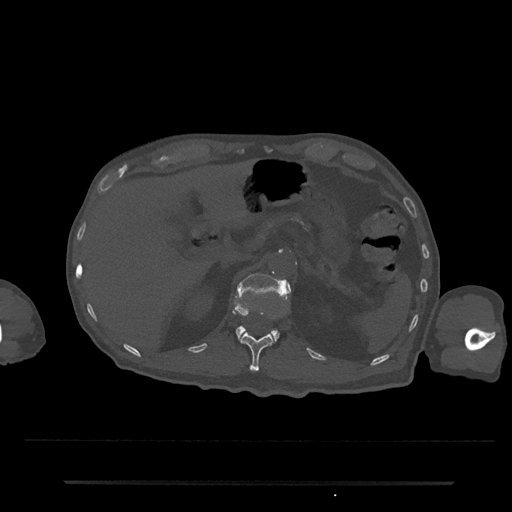
CT including the spine, one axial slice; slice 171 of 797 in the series (ordered by position); bone window (W 1800 / L 400 HU); 0.5 mm slice thickness; 512 × 512 image matrix, field of view 427 × 427 mm. Male patient, age 74 years. From the clinical record (not read from this slice): primary cancer: prostate.
Outlined on this slice (semi-automatic segmentation, software-assisted and operator-edited):
- L1 vertebra: box from (x=234, y=273) to (x=292, y=342) px
- T12 vertebra: (x=240, y=333)–(x=274, y=372)